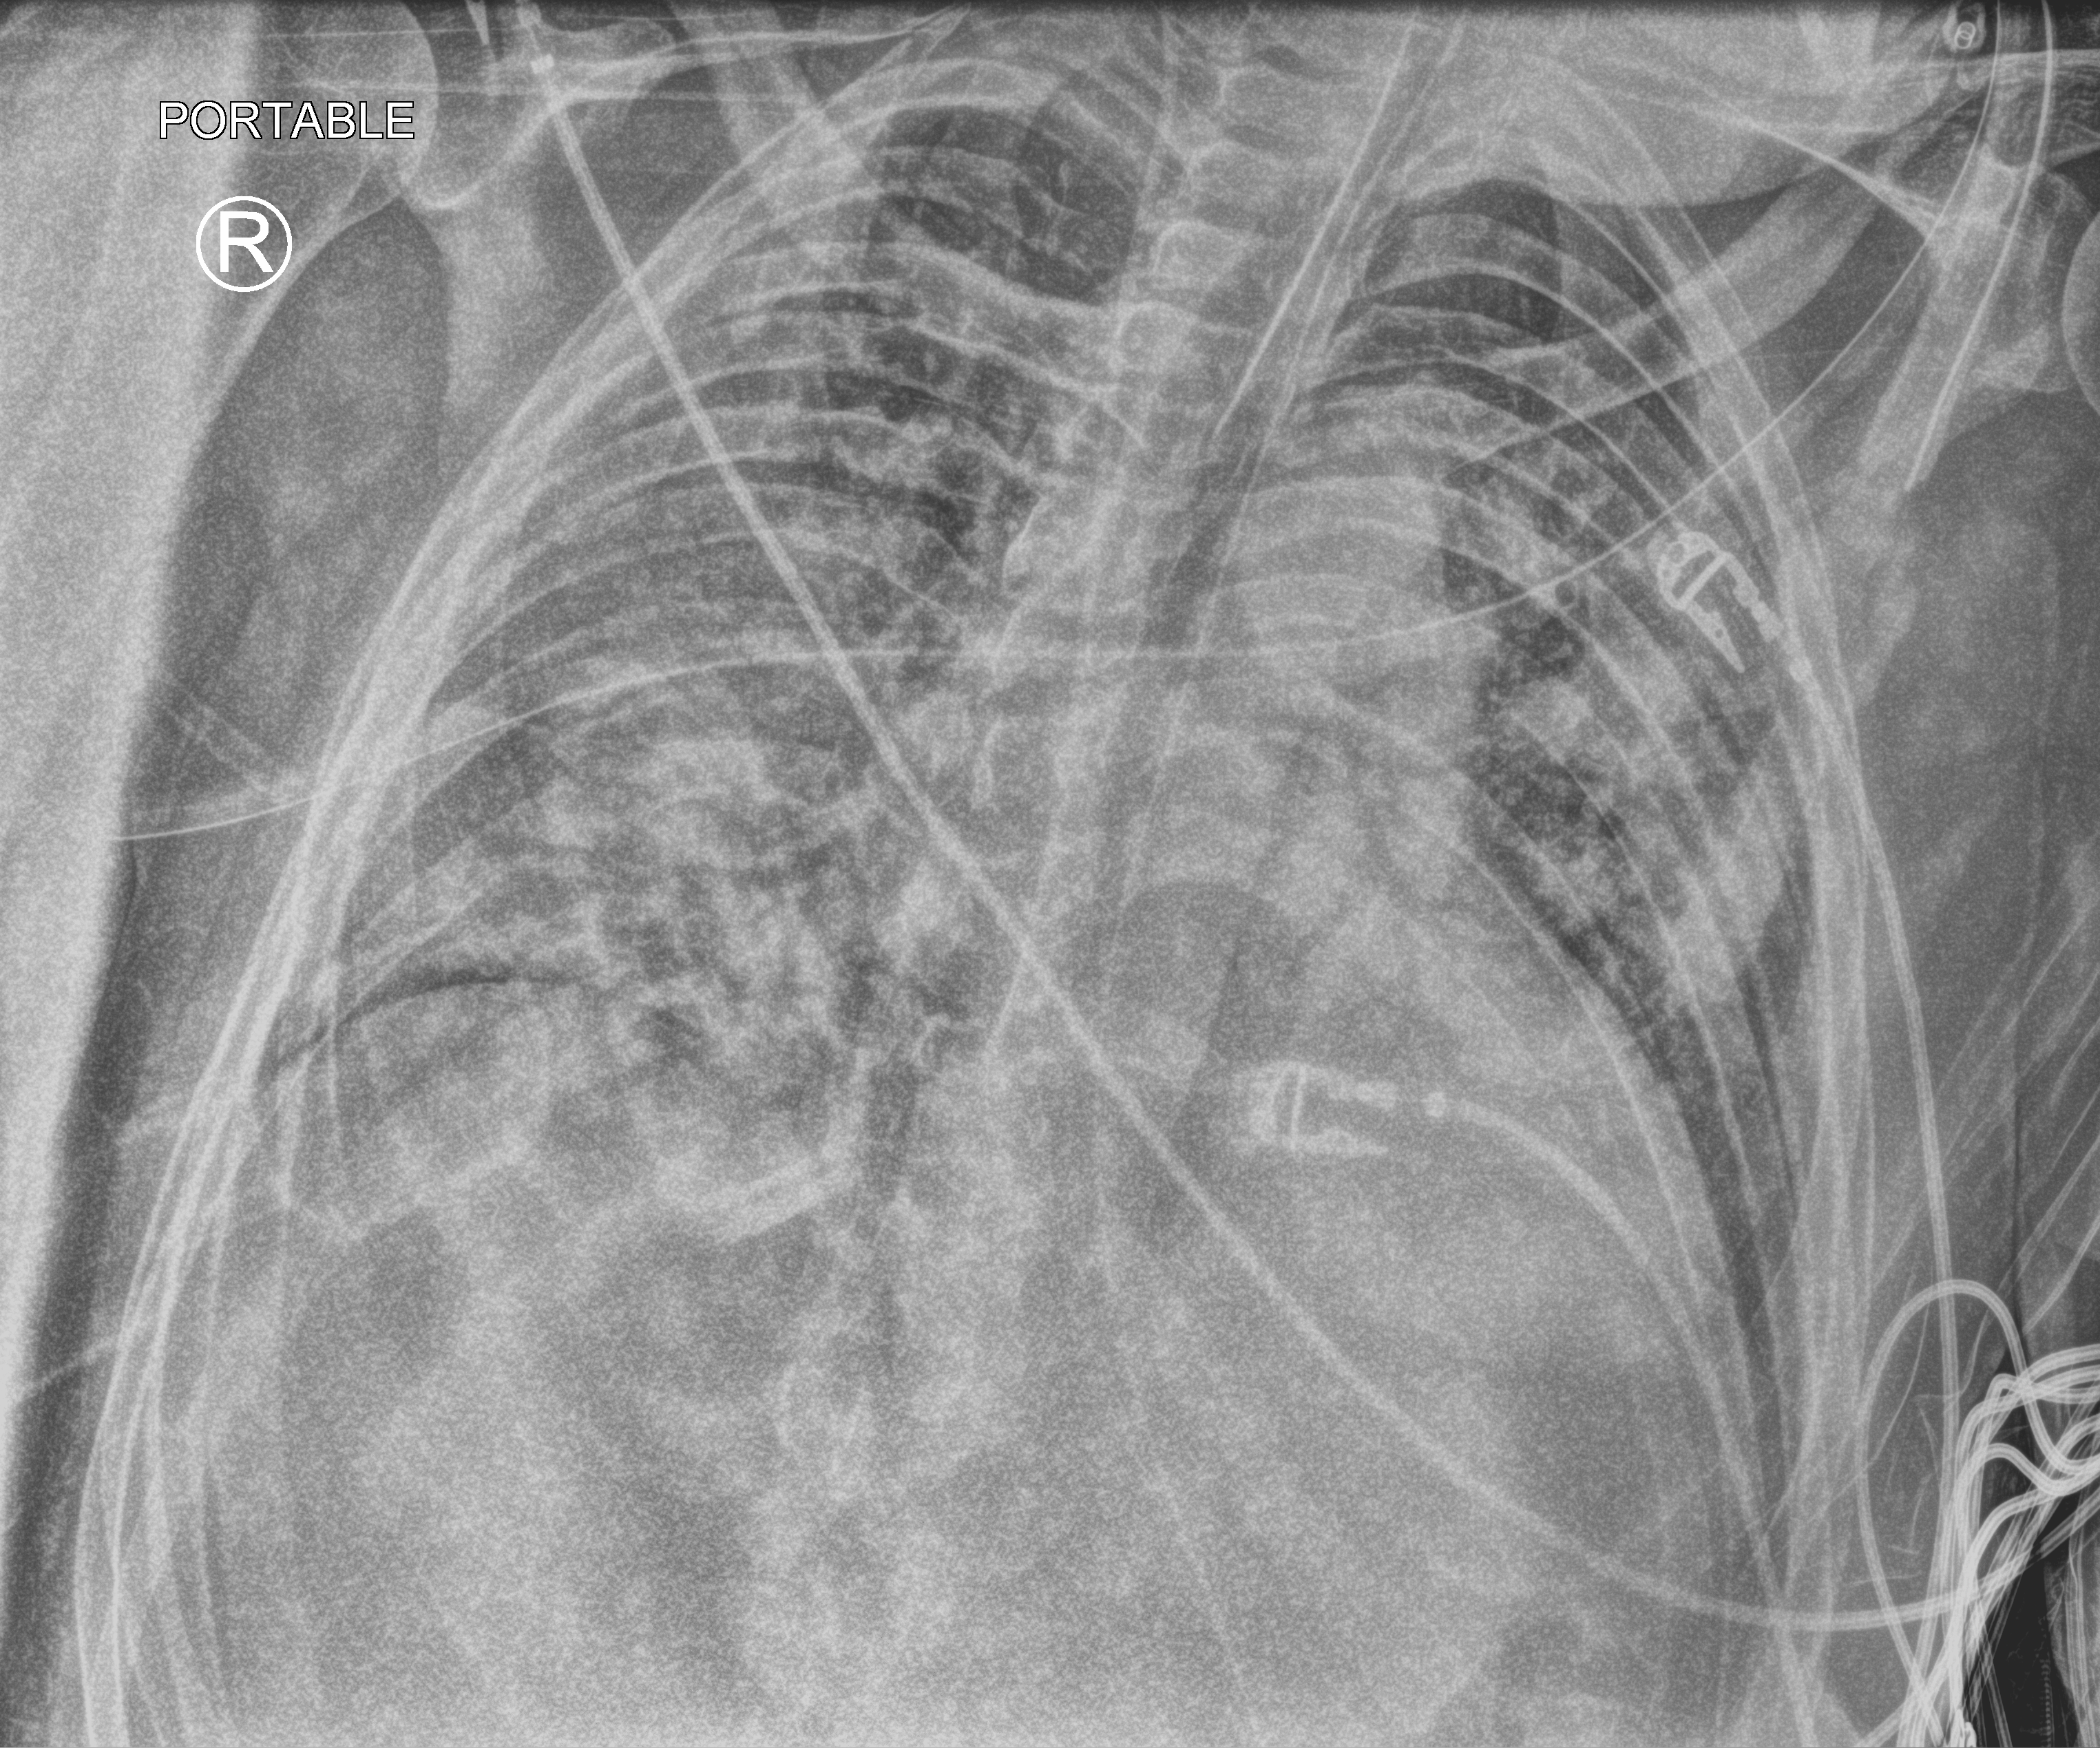
Portable chest radiograph, anteroposterior (AP) projection. Male patient hospitalised with COVID-19, age 18–59 years.
Hospital-stay facts (about this admission, not read from this image; timing relative to this image not recorded):
- admitted to intensive care during this hospital stay: yes
- mechanically ventilated during this hospital stay: yes